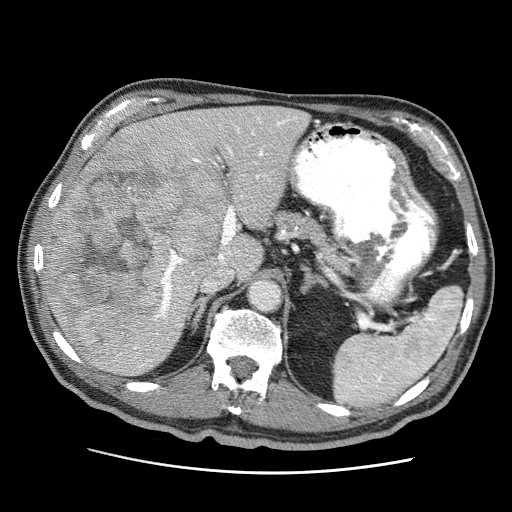
Contrast-enhanced abdominal CT (liver protocol), one axial slice. Position 32 of 75 along the scan axis. 120 kVp. Soft-tissue window (W 400 / L 40 HU). 2.5 mm slice thickness. 512 × 512 image matrix. From the clinical record (not read from this slice): diagnosis: hepatocellular carcinoma (patient treated with transarterial chemoembolisation; whether this scan precedes or follows treatment is not stated here); TNM stage (as recorded): Stage-IIIA; Child-Pugh class: A; tumour differentiation: well differentiated.
Outlined on this slice (semi-automatic segmentation, software-assisted and operator-edited):
- liver parenchyma outside the tumour (the mass and vessels are separate outlines, so this box may not span the whole liver): bounding box <42,106,309,376> (left, top, right, bottom; pixels)
- mass: <48,136,231,369>
- liver vessels: <134,116,298,368>